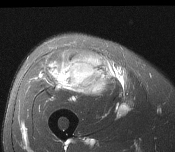
MRI of an extremity soft-tissue mass, one axial slice; position 74 of 116 along the scan axis; T2-weighted fat-saturated; MR volume resampled by the dataset authors to the PET/CT grid (not the native acquisition matrix); 3.27 mm slice thickness; 175 × 152 image matrix. Male patient. Case-level facts recorded for this patient, not image findings: histological type: pleiomorphic leiomyosarcoma; grade: intermediate; site of the primary tumour: right thigh.
Structures marked on this image (expert contour drawn on MRI and transferred to this co-registered scan by the dataset authors):
- gross tumour volume including surrounding oedema: box from (x=51, y=51) to (x=109, y=98) px
- gross tumour volume (mass): (x=51, y=52)–(x=109, y=96)